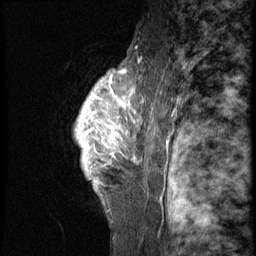
Breast MRI (dynamic contrast-enhanced), one sagittal slice; 3 images stored at this slice position (order not interpretable as contrast timing); 1.5 T; TE 4.2 ms, TR 9 ms; 2.5 mm slice thickness; 256 × 256 image matrix. Patient: female, 50 years. From the clinical record (not read from this slice): setting: breast cancer imaged before/during neoadjuvant chemotherapy; receptor status: triple-negative.
Outlined on this slice (semi-automatically segmented with operator editing):
- analysis volume of interest (the breast-tissue region the enhancement analysis was run in; not a lesion): bounding box [x1, y1, x2, y2] px = [67, 63, 127, 214]
- tumour enhancement mask (voxels above the 140 % enhancement threshold inside the analysis volume of interest): [76, 70, 127, 179]